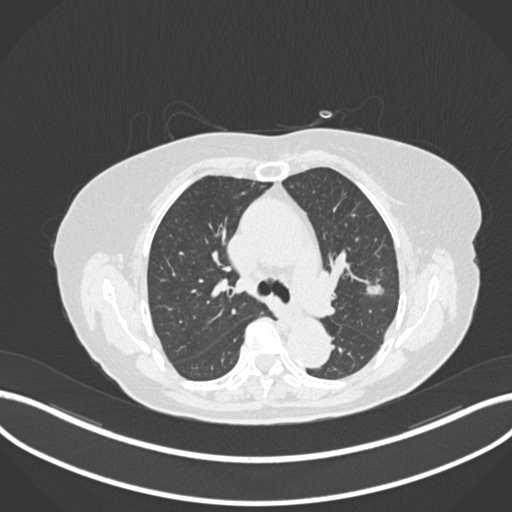
Chest CT, one axial slice; slice 106 of 168 in the series (ordered by position); reconstruction kernel B30f; lung window (W 1500 / L -600 HU); 512 × 512 image matrix, field of view 400 × 400 mm. Female patient, age 75 years. Case-level facts recorded for this patient, not image findings: clinical TNM (as recorded): T1c N0 M0.
Annotated regions visible in this slice (bounding box drawn by a radiologist):
- lung tumour (recorded histology: adenocarcinoma): bounding box (x1, y1, x2, y2) in pixels: (366, 282, 385, 298)